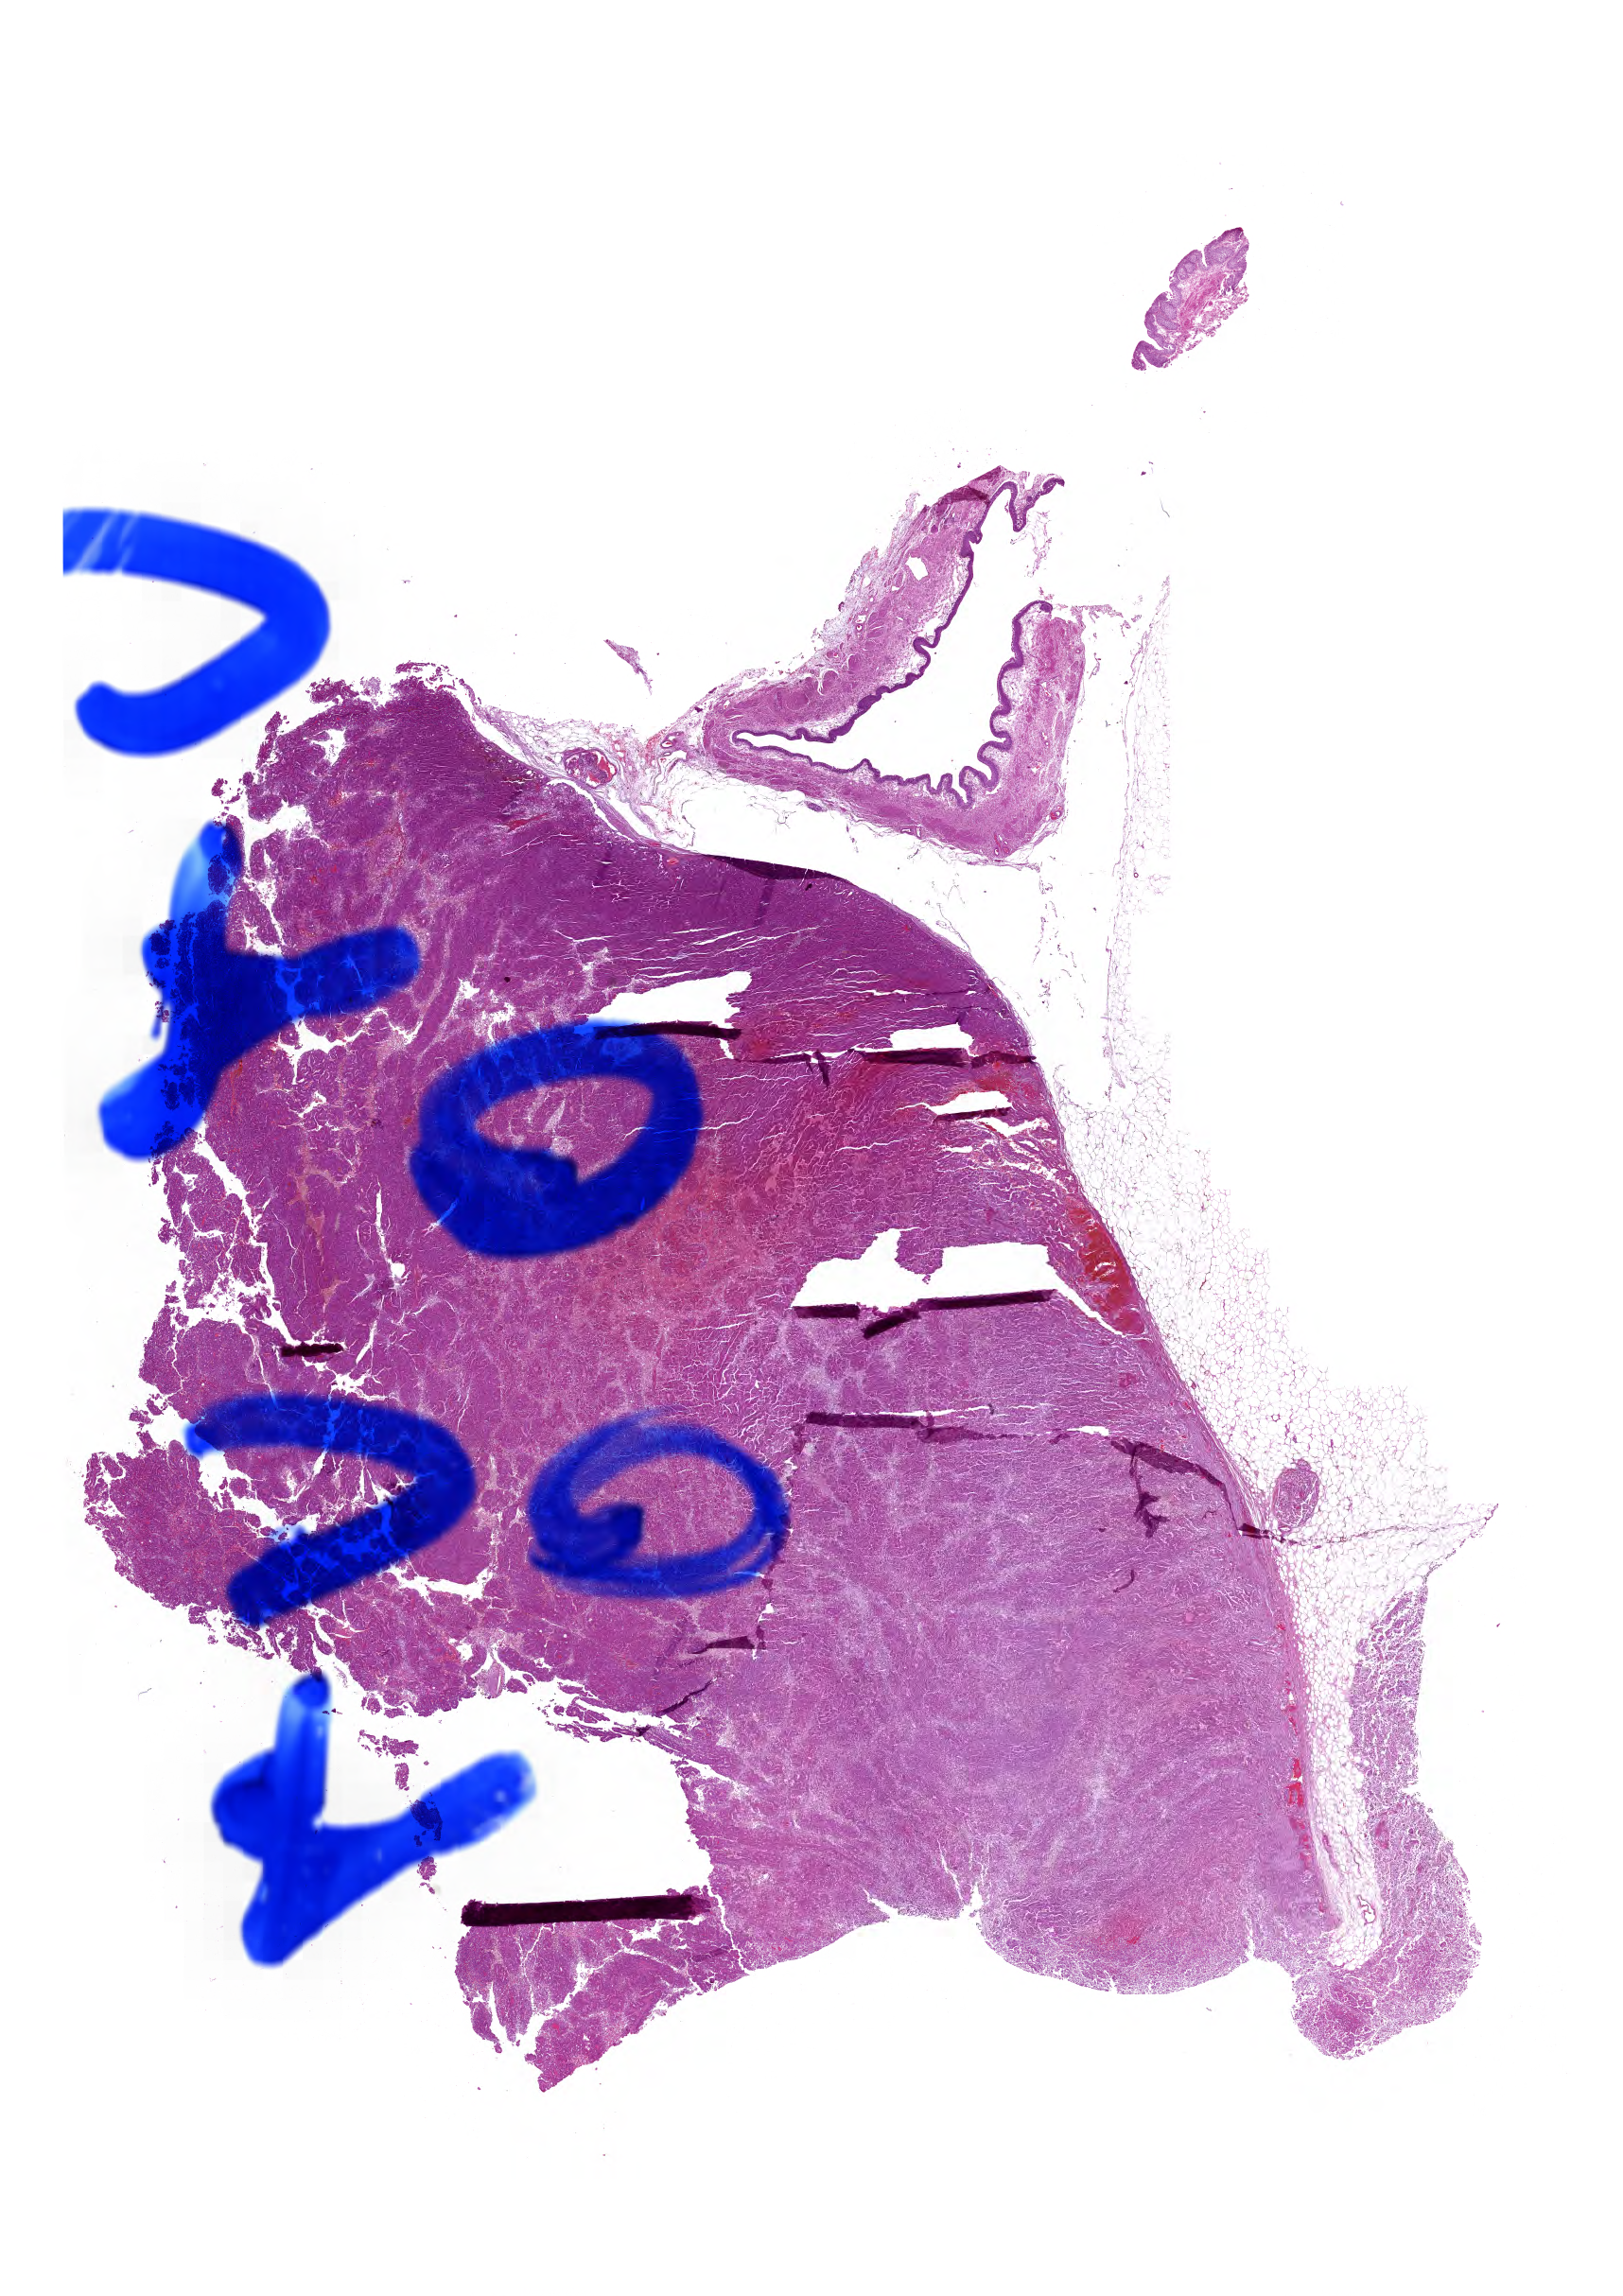
Digitized H&E tissue section (whole slide) — a low-resolution overview of the entire scanned area, about 21.4 x 30.2 mm; FFPE section; kidney, primary tumour sample. Patient: male, age at initial diagnosis 81 years.
Pathologic diagnosis: Papillary adenocarcinoma, NOS. AJCC pathologic stage: III. Laterality: left.